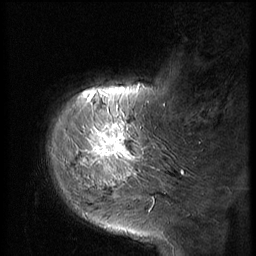
Breast MRI (dynamic contrast-enhanced), one sagittal slice. Position 12 of 56 along the scan axis. Dynamic contrast-enhanced series, image 2 of 2 at this slice position (ordered by acquisition). 1.5 T. TE 4.2 ms, TR 9 ms. 2.5 mm slice thickness. 256 × 256 image matrix, field of view 180 × 180 mm. Female patient, age 51 years. Case-level facts recorded for this patient, not image findings: setting: breast cancer imaged before/during neoadjuvant chemotherapy; receptor status: triple-negative.
Outlined on this slice (semi-automatic segmentation, software-assisted and operator-edited):
- analysis volume of interest (the breast-tissue region the enhancement analysis was run in; not a lesion): bounding box (x1, y1, x2, y2) in pixels: (60, 98, 147, 197)
- tumour enhancement mask (voxels above the 140 % enhancement threshold inside the analysis volume of interest): (84, 98, 133, 173)